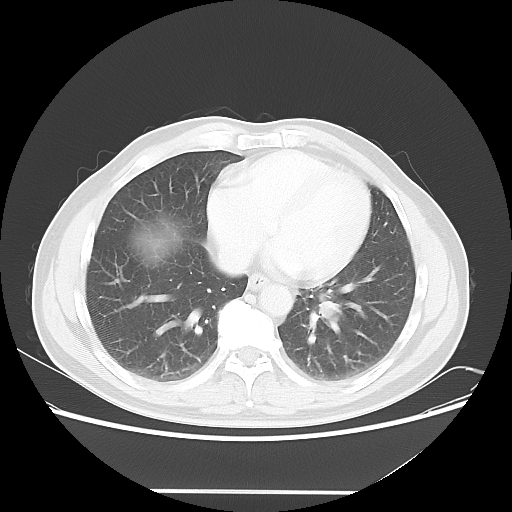
Chest CT, one axial slice; reconstruction kernel LUNG; 120 kVp; lung window (W 1500 / L -600 HU); 5 mm slice thickness; 512 × 512 image matrix. Patient: male, 61 years. Case-level facts recorded for this patient, not image findings: clinical TNM (as recorded): T1c N0 M0.
Structures marked on this image (bounding box drawn by a radiologist):
- lung tumour (recorded histology: adenocarcinoma): bounding box (x1, y1, x2, y2) in pixels: (315, 289, 345, 327)